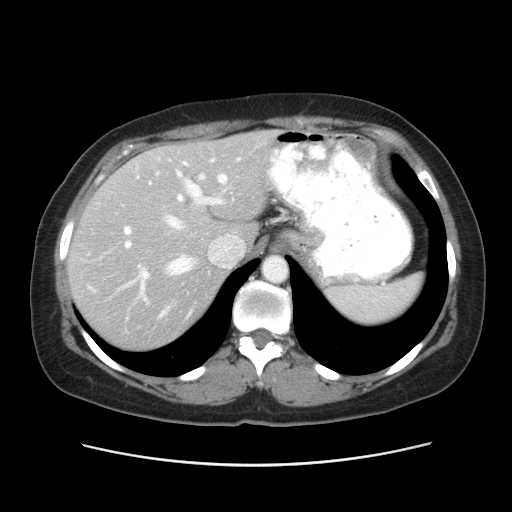
Contrast-enhanced abdominal CT, one axial slice. Position 39 of 52 along the scan axis. 120 kVp. Intravenous contrast given. Soft-tissue window (W 400 / L 40 HU). 5 mm slice thickness. 512 × 512 image matrix, field of view 362 × 362 mm. Female patient, age 48 years. Case-level facts recorded for this patient, not image findings: diagnosis: colorectal cancer liver metastases, imaged before liver resection; multiple liver metastases: yes; largest metastasis: 4.5 cm; chemotherapy before resection: yes.
Annotated regions visible in this slice (expert manual segmentation):
- hepatic veins: bounding box [x1, y1, x2, y2] px = [122, 157, 241, 316]
- liver: [70, 132, 272, 348]
- planned liver remnant (the part of the liver to remain after resection): [145, 132, 272, 242]
- portal vein (with intrahepatic branches): [124, 159, 222, 290]